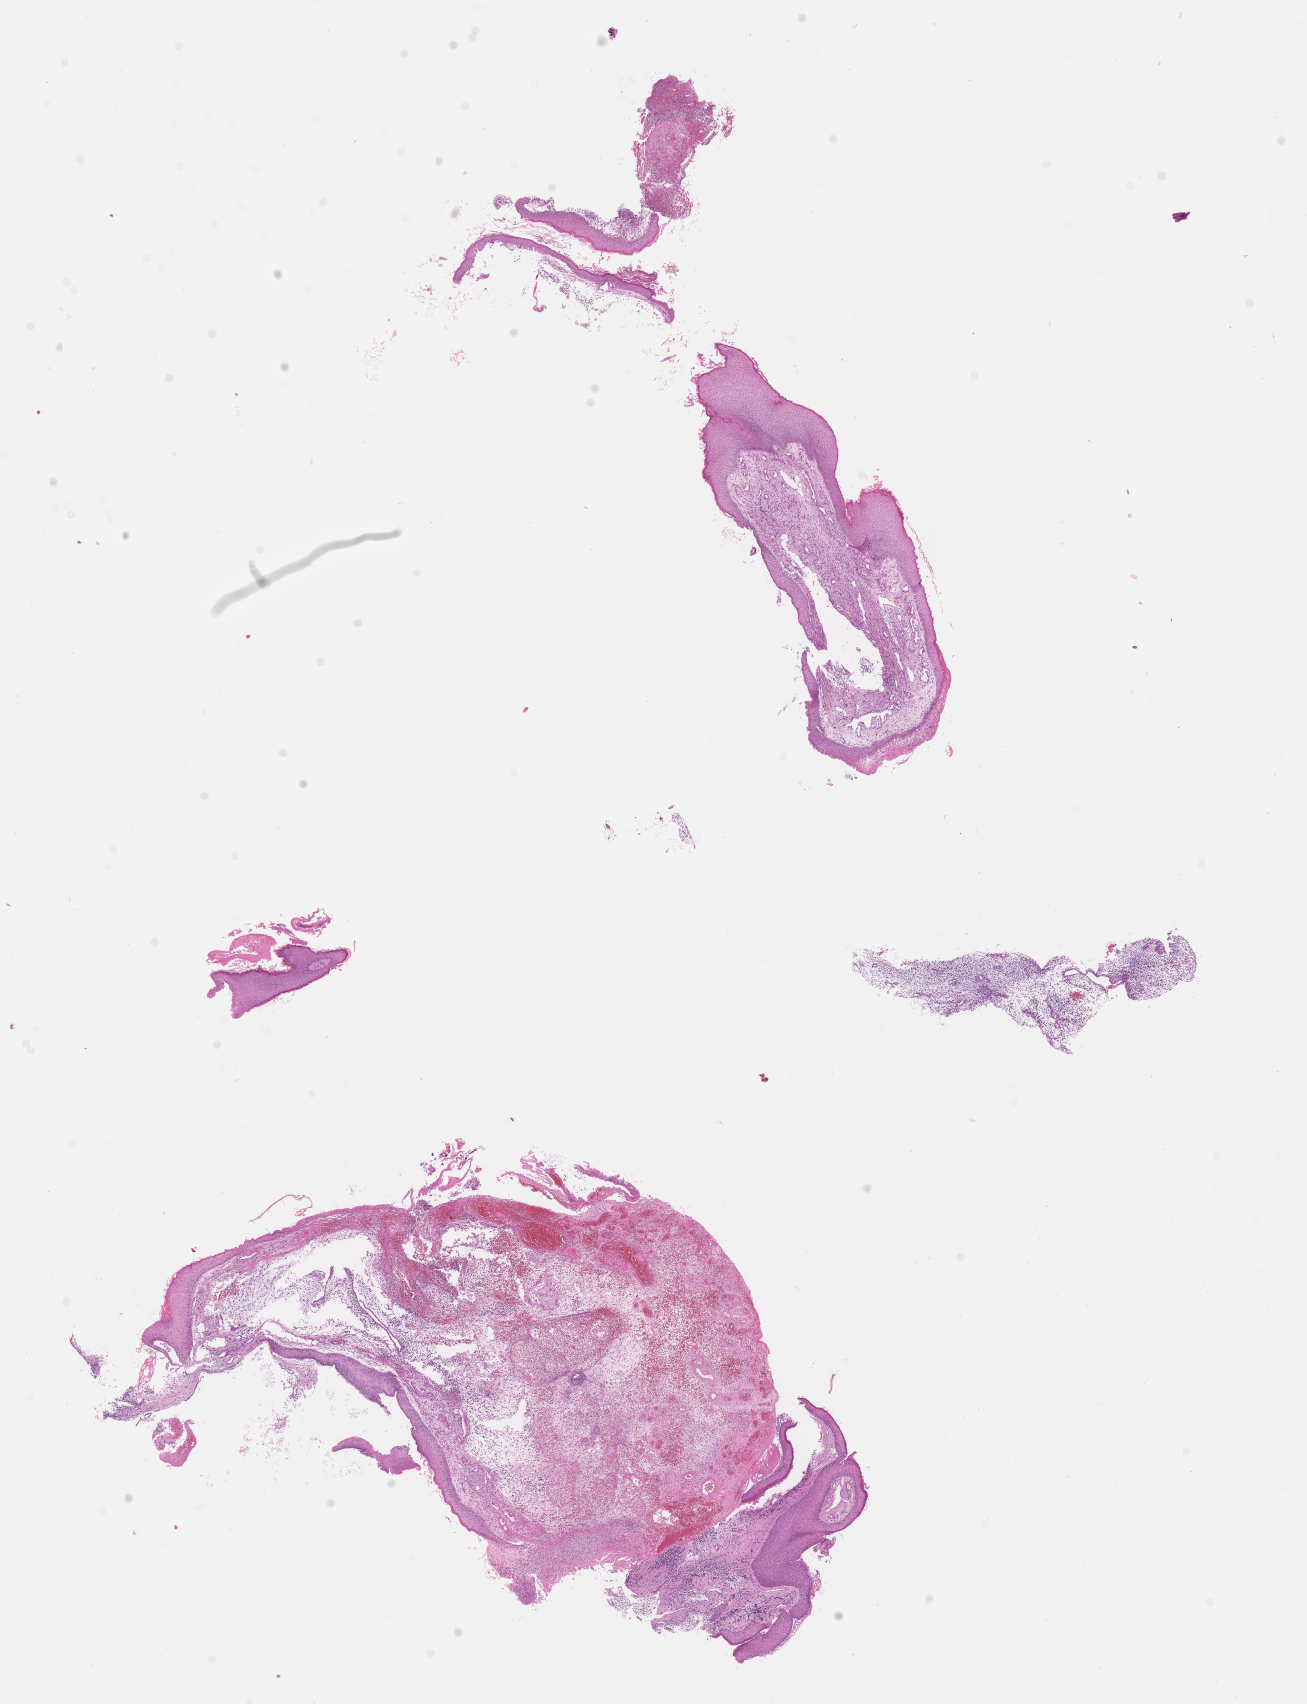
Digitized H&E-stained section of tumor tissue, whole scanned area (about 10.6 x 13.8 mm) shown as a low-resolution overview, FFPE section, sample anatomic site: soft tissue, ear-left. Male patient, age at diagnosis 5.6 years.
- stage (as recorded): 4
- primary site (case record): middle Ear
- diagnosis: rhabdomyosarcoma; histological classification: embryonal rhabdomyosarcoma
- metastatic status at presentation (as recorded): metastatic